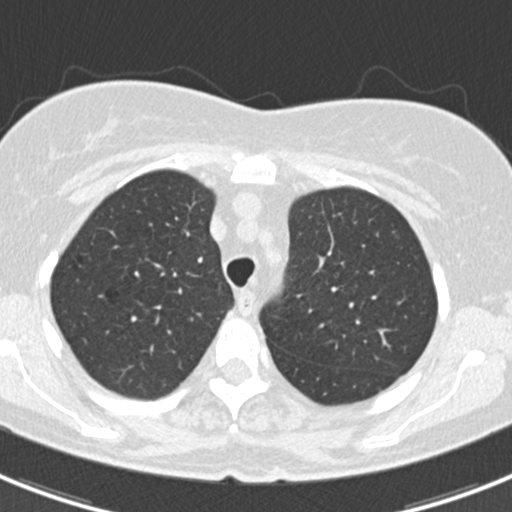
Low-dose screening chest CT, axial slice; baseline annual screen; lung window (W 1500 / L -600 HU); standard (soft-tissue) reconstruction kernel (B30f); slice 48 of 184 in the series; 512 × 512 image matrix, field of view 298 × 298 mm. Female participant, aged 60 years at enrolment.
Expert reader's lesion annotation, bounding box <377,226,421,268> (left, top, right, bottom; pixels). The screening reader recorded 3 non-calcified nodules or masses ≥4 mm on this exam (lingula, left lower lobe, lingula); which of them this box marks is not recorded. Official screen result: positive, change unspecified: nodule(s) >= 4 mm or enlarging nodule(s), mass(es), or other non-specific abnormalities suspicious for lung cancer. Participant outcome: lung cancer diagnosed 886 days after this screen (after the third annual screen) — non-small cell carcinoma, left upper lobe, poorly differentiated (G3), stage IB (AJCC 6th edition), 7 mm at pathology.